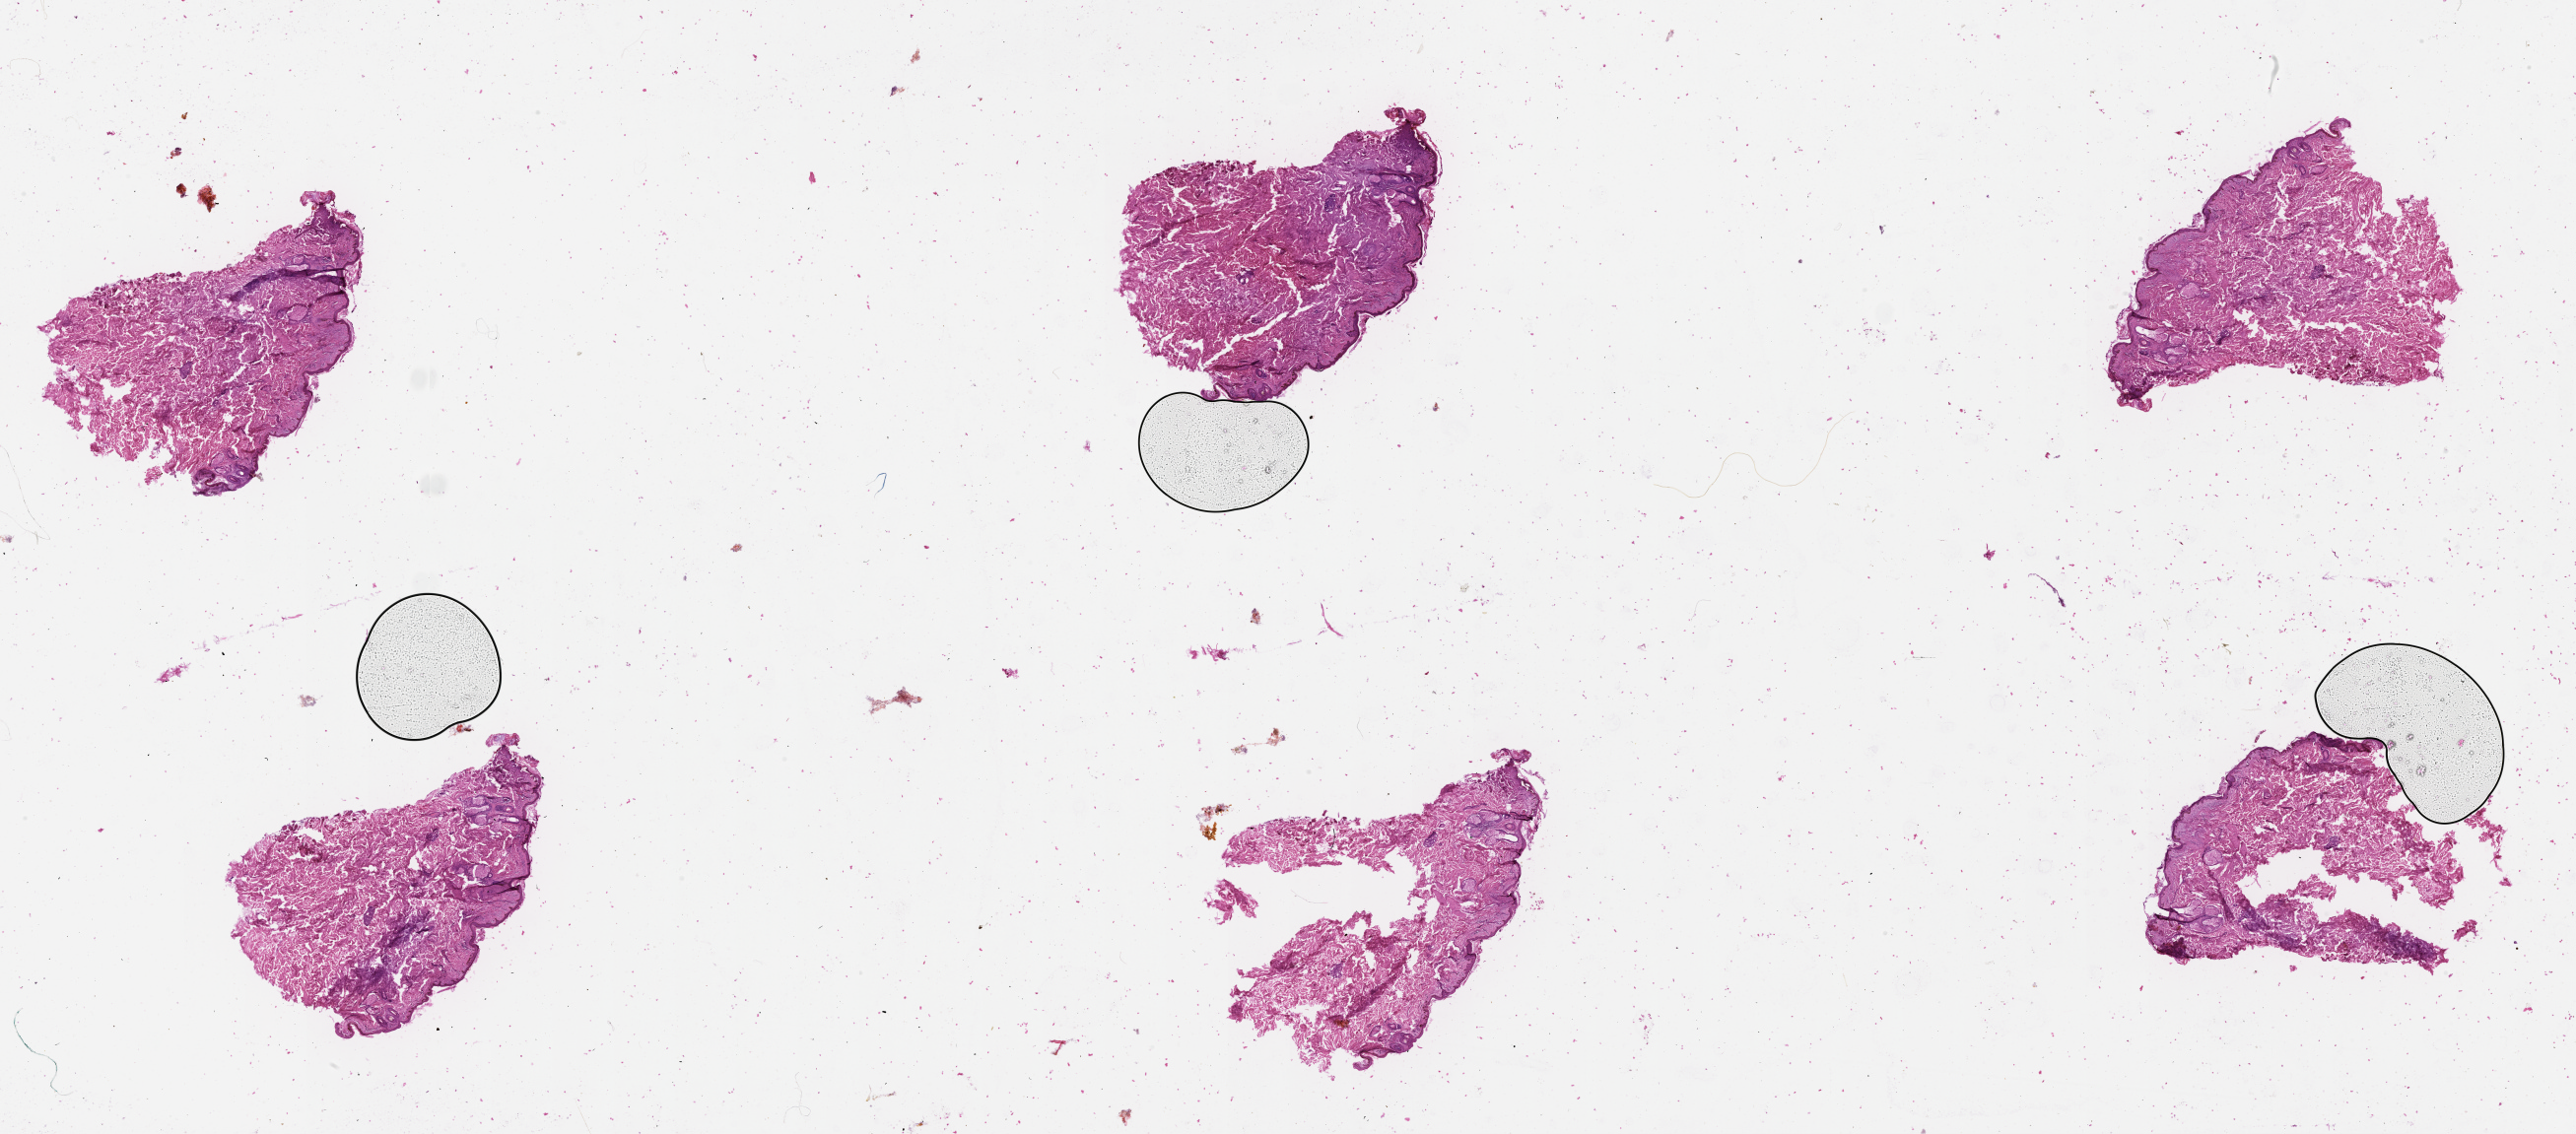
Hematoxylin and eosin (H&E) stained whole-slide image, low-resolution overview of the scanned area, about 42.1 x 18.5 mm.
Patient diagnosis (cohort enrolment): cutaneous melanoma (skin).